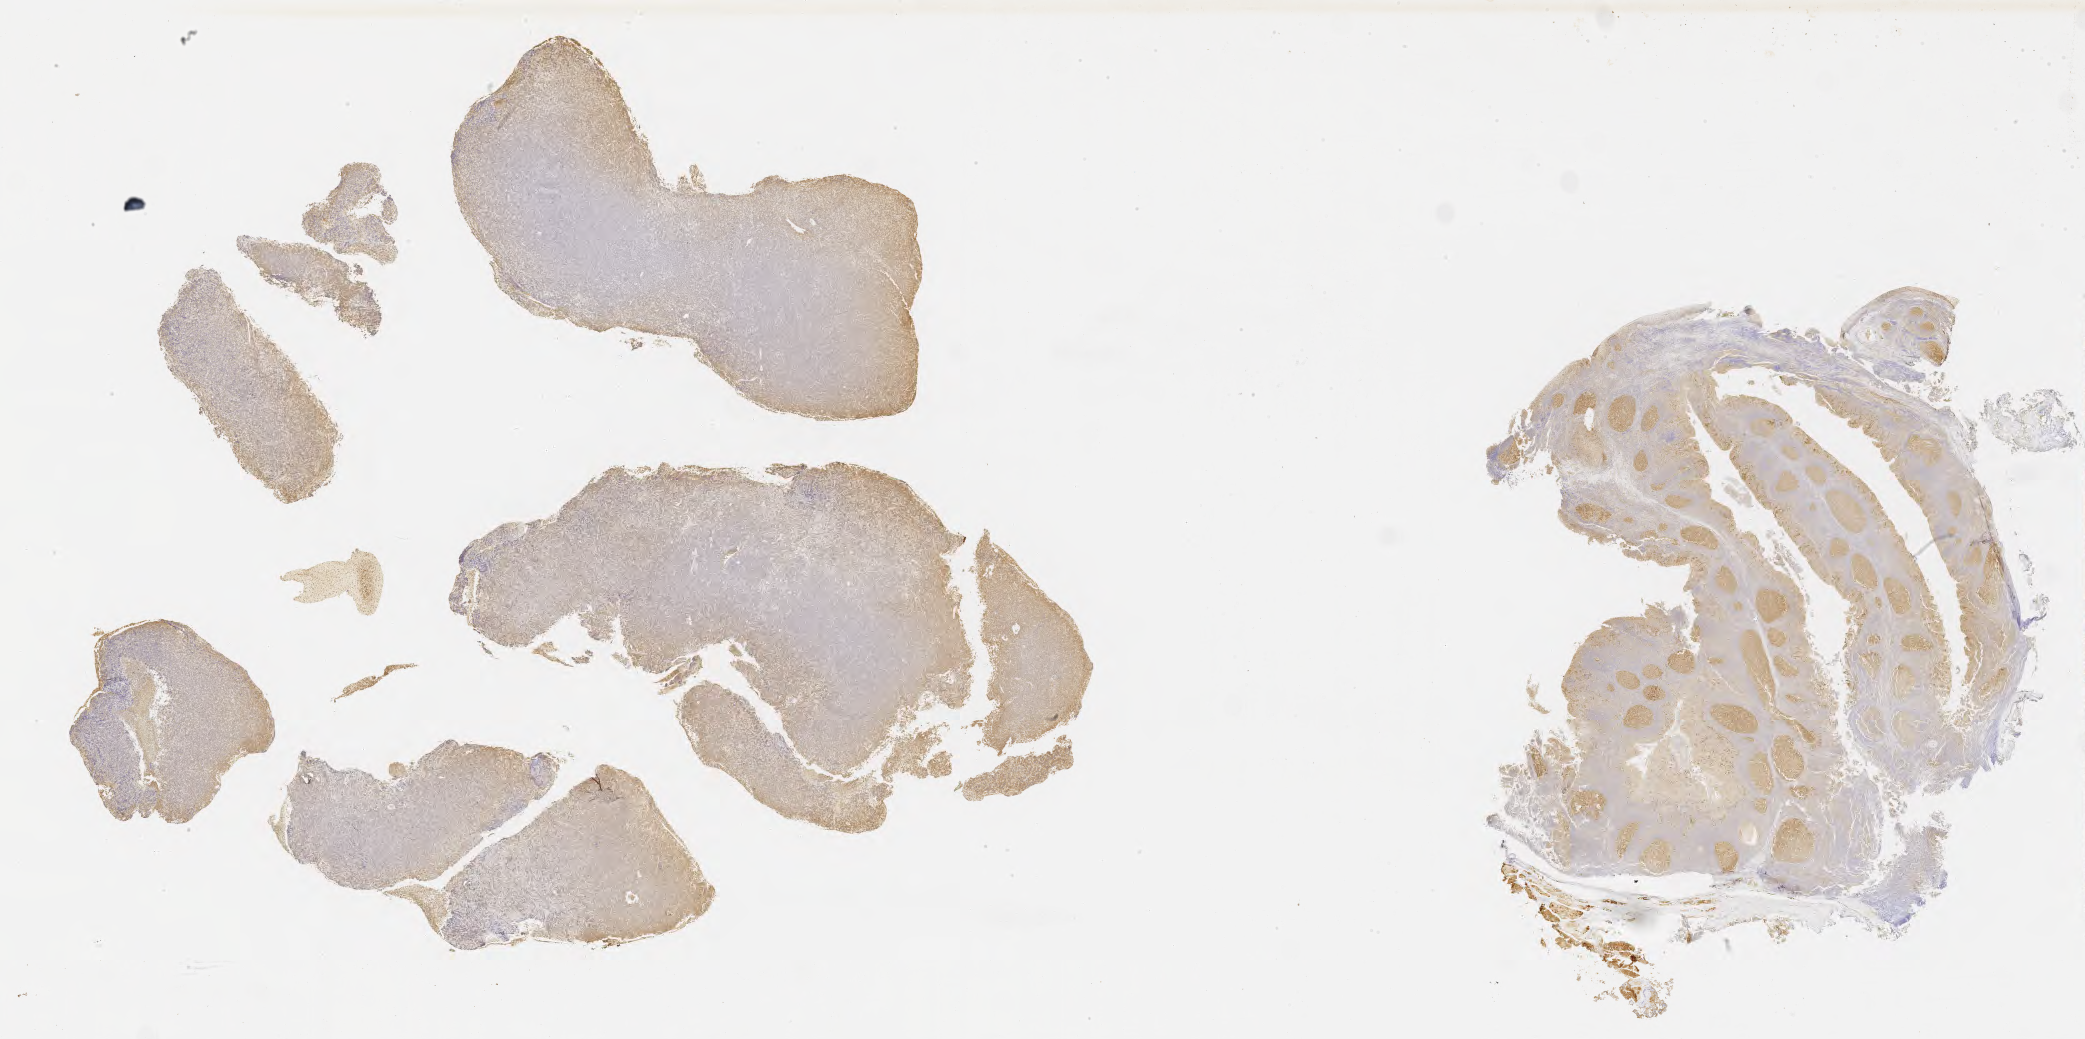
IHC for BCL6, whole-slide image, a low-resolution overview of the entire scanned area, about 33.7 x 16.8 mm; specimen: tumor tissue; site: soft tissue. Female, age 9 years at initial diagnosis.
Diagnosis: Burkitt lymphoma, NOS.